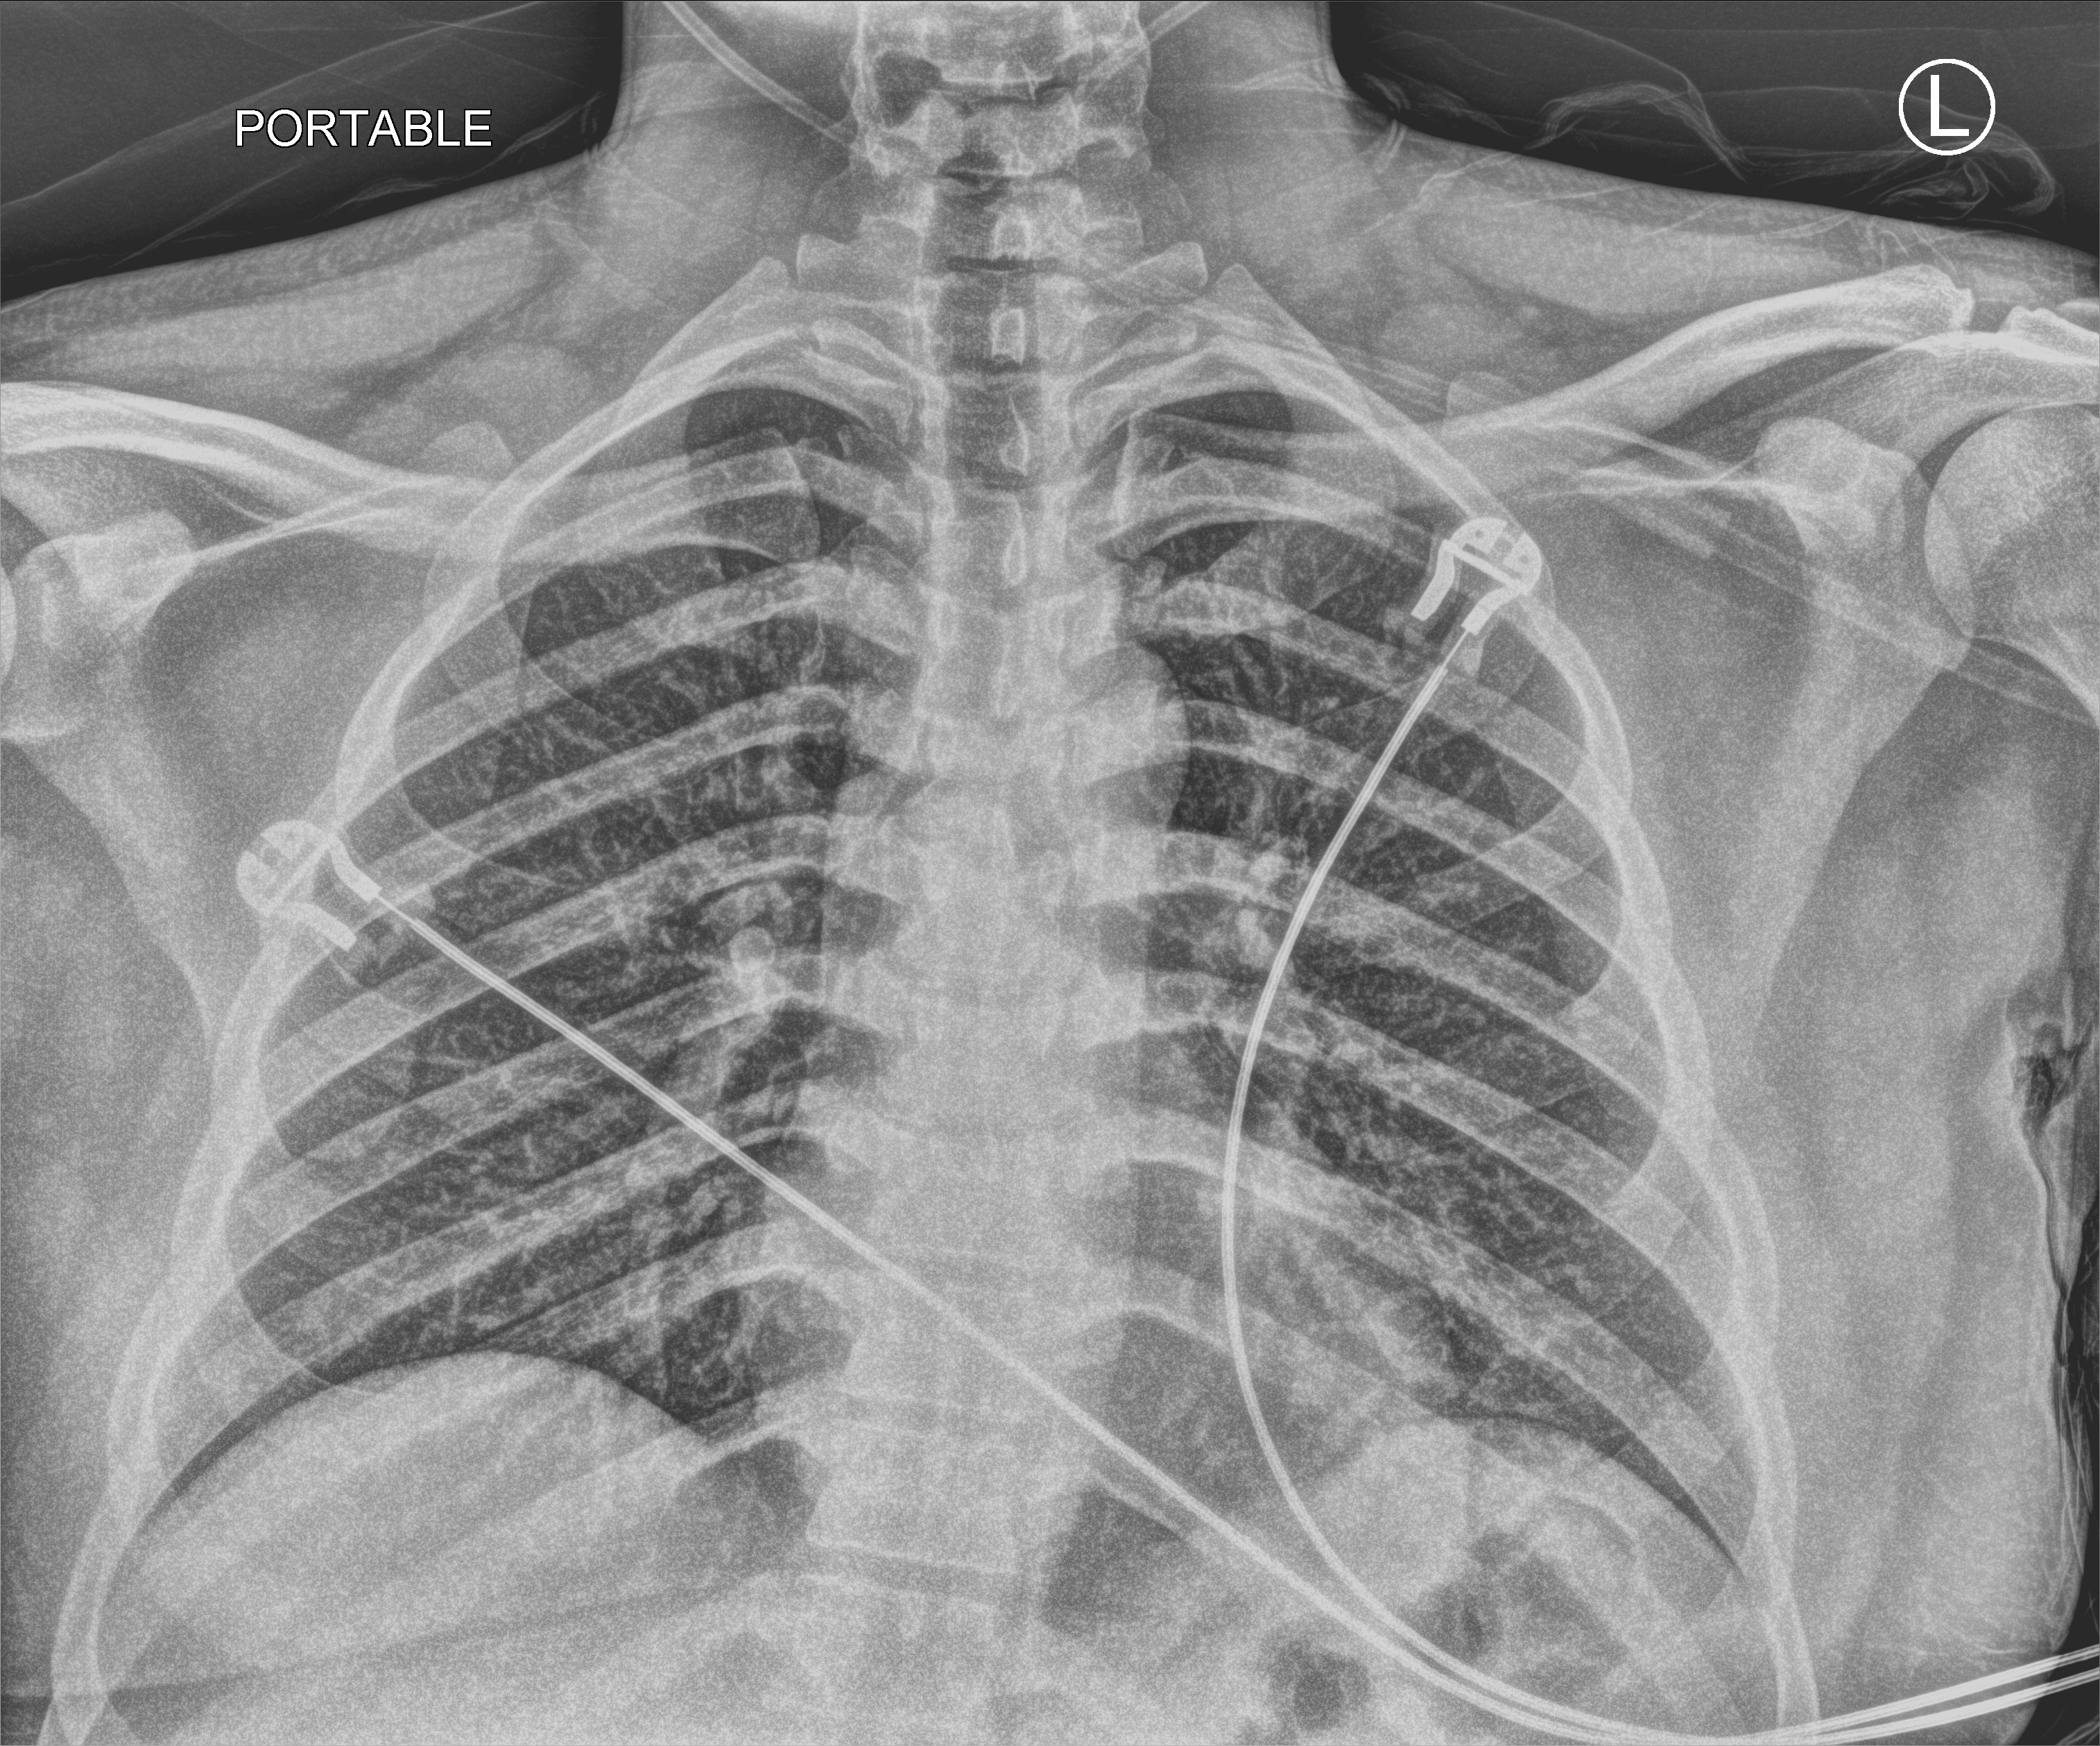
Portable chest radiograph; anteroposterior (AP) projection. Patient hospitalised with COVID-19; male, aged 18–59 years.
Admission-level facts for this patient (not findings on this image; timing relative to this image not recorded):
- mechanically ventilated during this hospital stay: no